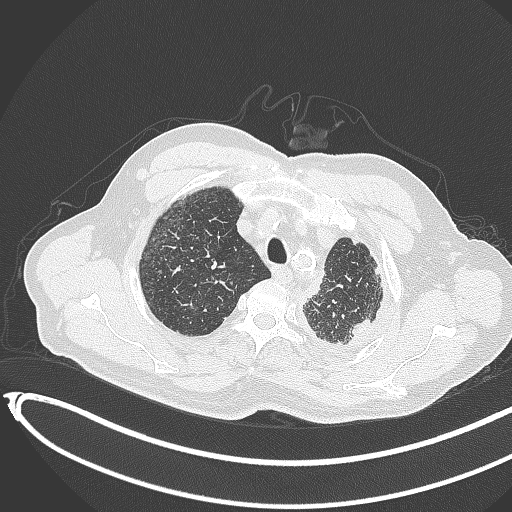
Chest CT, one axial slice; reconstruction kernel B70f; 120 kVp; lung window (W 1500 / L -600 HU); 1 mm slice thickness; 512 × 512 image matrix, field of view 400 × 400 mm. Male patient, age 78 years. From the clinical record (not read from this slice): clinical TNM (as recorded): T1c N0 M1.
Structures marked on this image (bounding box drawn by a radiologist):
- lung tumour (recorded histology: adenocarcinoma): bounding box (x1, y1, x2, y2) in pixels: (346, 312, 373, 343)